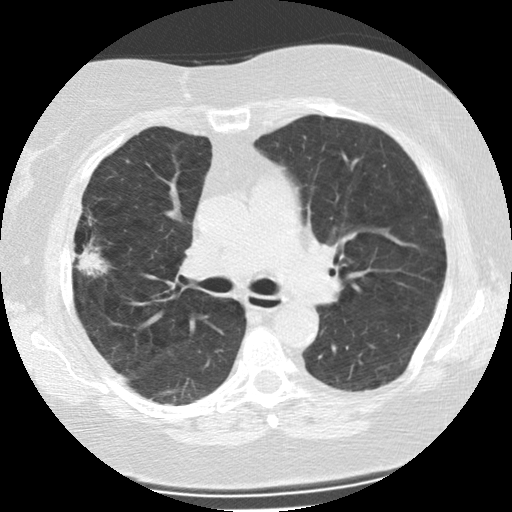
Low-dose screening chest CT, one axial slice. Position 142 of 225 along the scan axis. Reconstruction kernel STANDARD. Lung window (W 1500 / L -600 HU). 512 × 512 image matrix, field of view 320 × 320 mm.
Structures marked on this image (manually delineated by an expert):
- lesion 1 (tumor, upper lobe of right lung): bounding box [x1, y1, x2, y2] px = [76, 241, 108, 276]